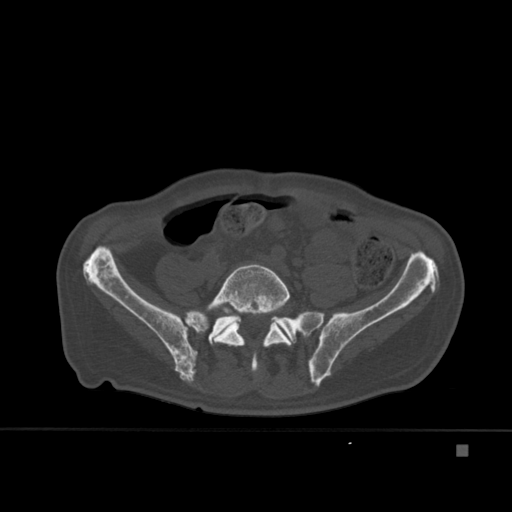
CT including the spine, one axial slice; position 99 of 451 along the scan axis; bone window (W 1800 / L 400 HU); 1.5 mm slice thickness; 512 × 512 image matrix. Male patient, age 75 years. From the clinical record (not read from this slice): primary cancer: prostate.
Annotated regions visible in this slice (semi-automatically segmented with operator editing):
- L5 vertebra: bounding box [x1, y1, x2, y2] px = [196, 264, 292, 372]
- T7 vertebra: [216, 301, 244, 340]